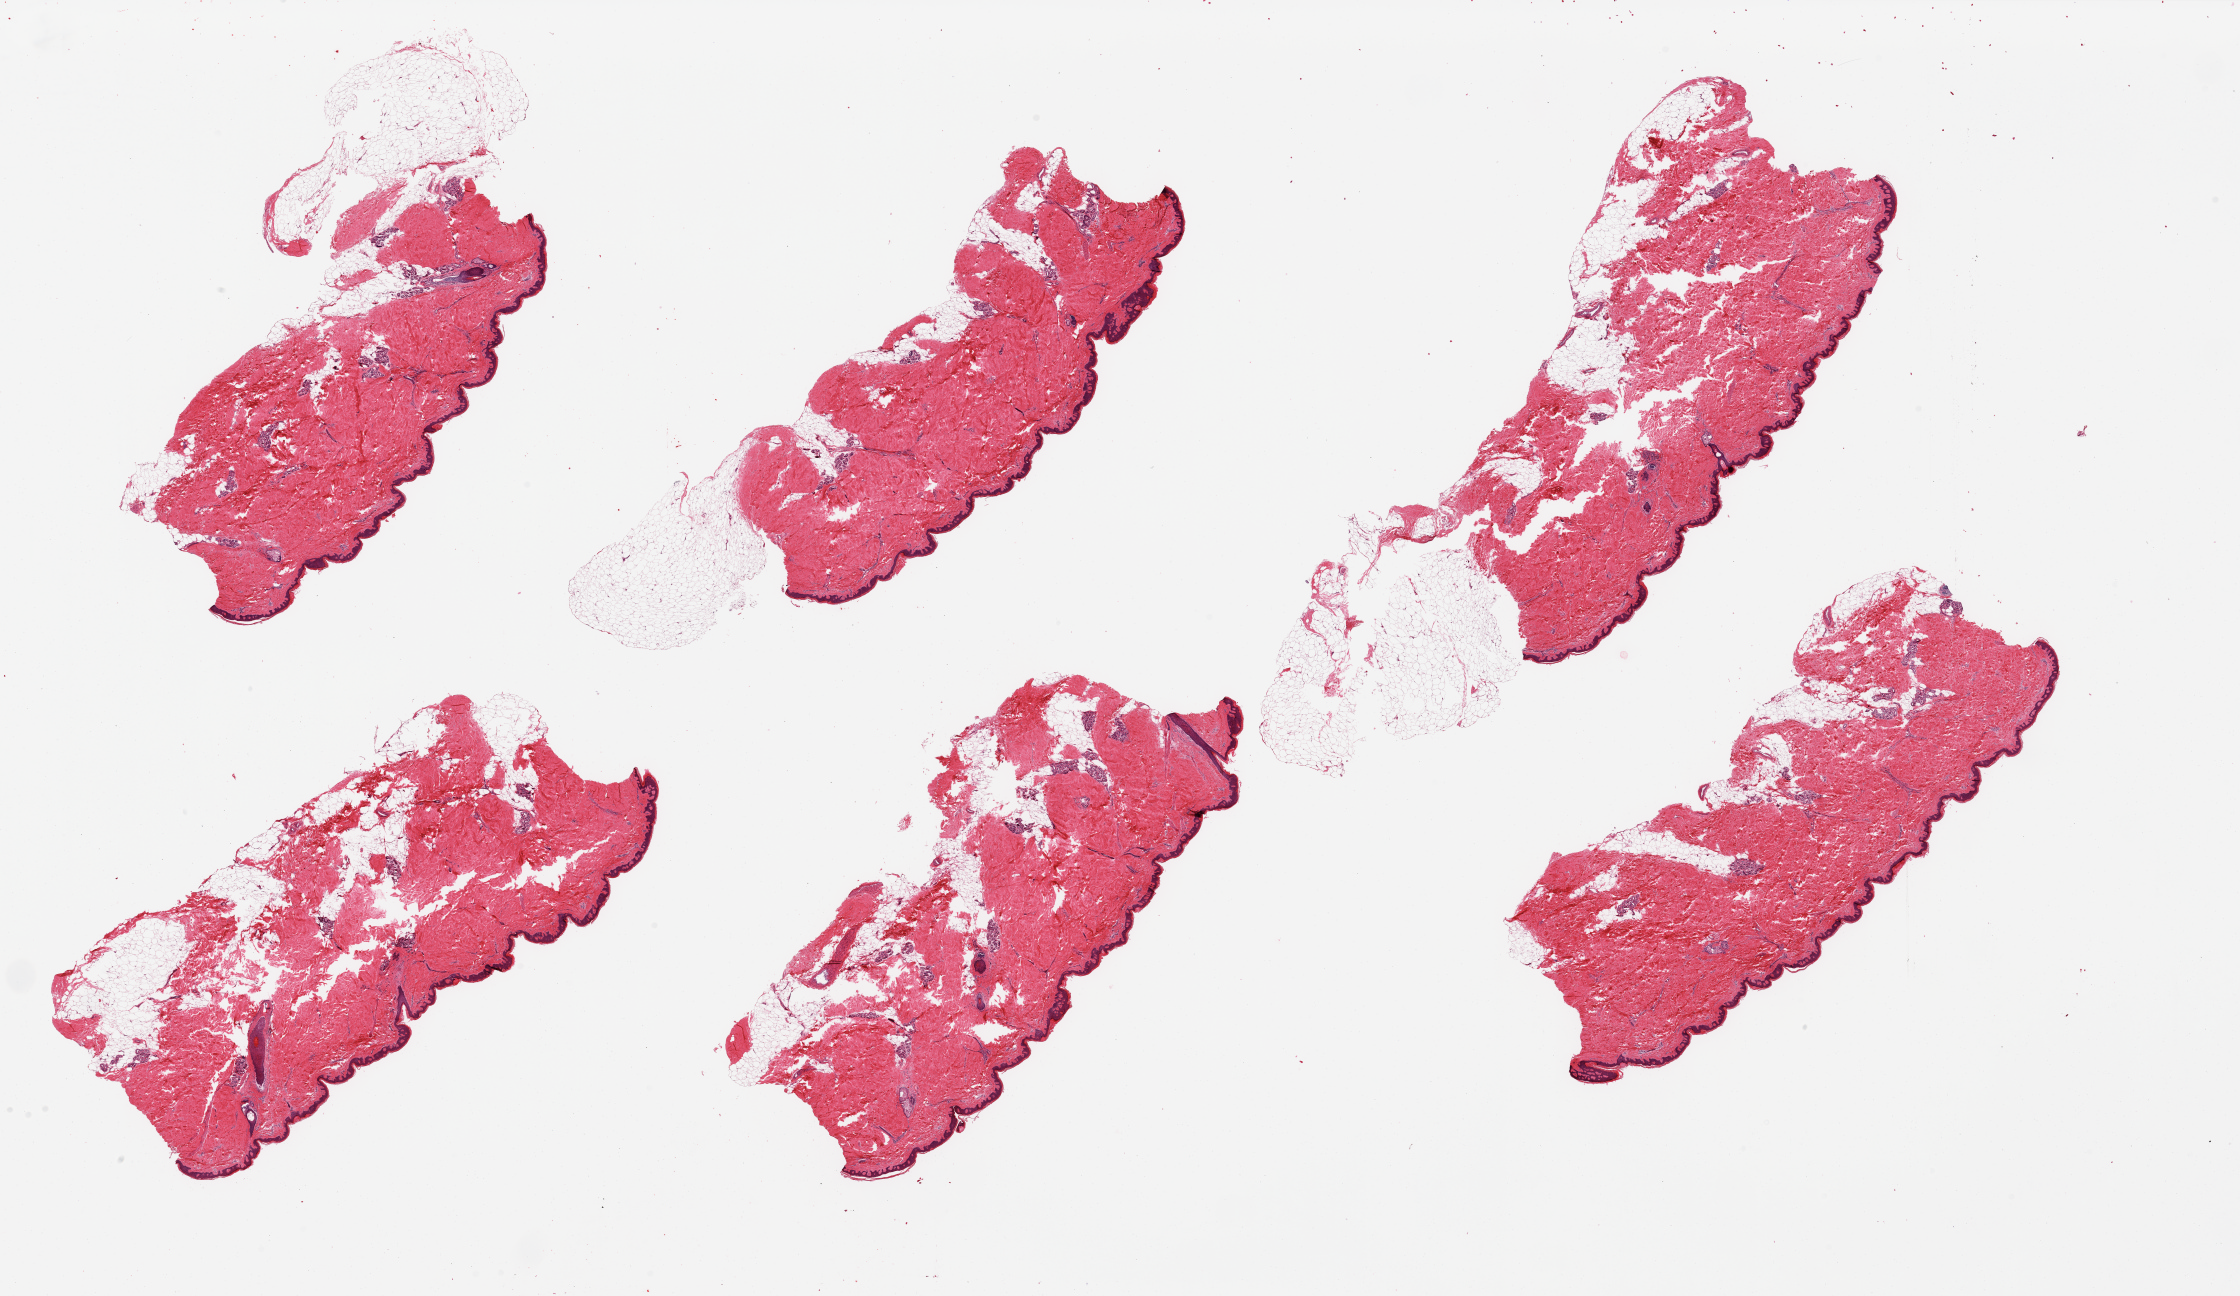
Whole-slide image, haematoxylin and eosin stain, brightfield, a low-resolution overview of the entire scanned area, about 35.4 x 20.5 mm (acquisition: 20x scan). PAXgene-fixed paraffin-embedded (PFPE) section. Sampled site (target tissue): skin of lower leg. Tissue donor sample.
Review note (as recorded): 6 pieces; up to 4 mm extraneous subcutaneous fat.